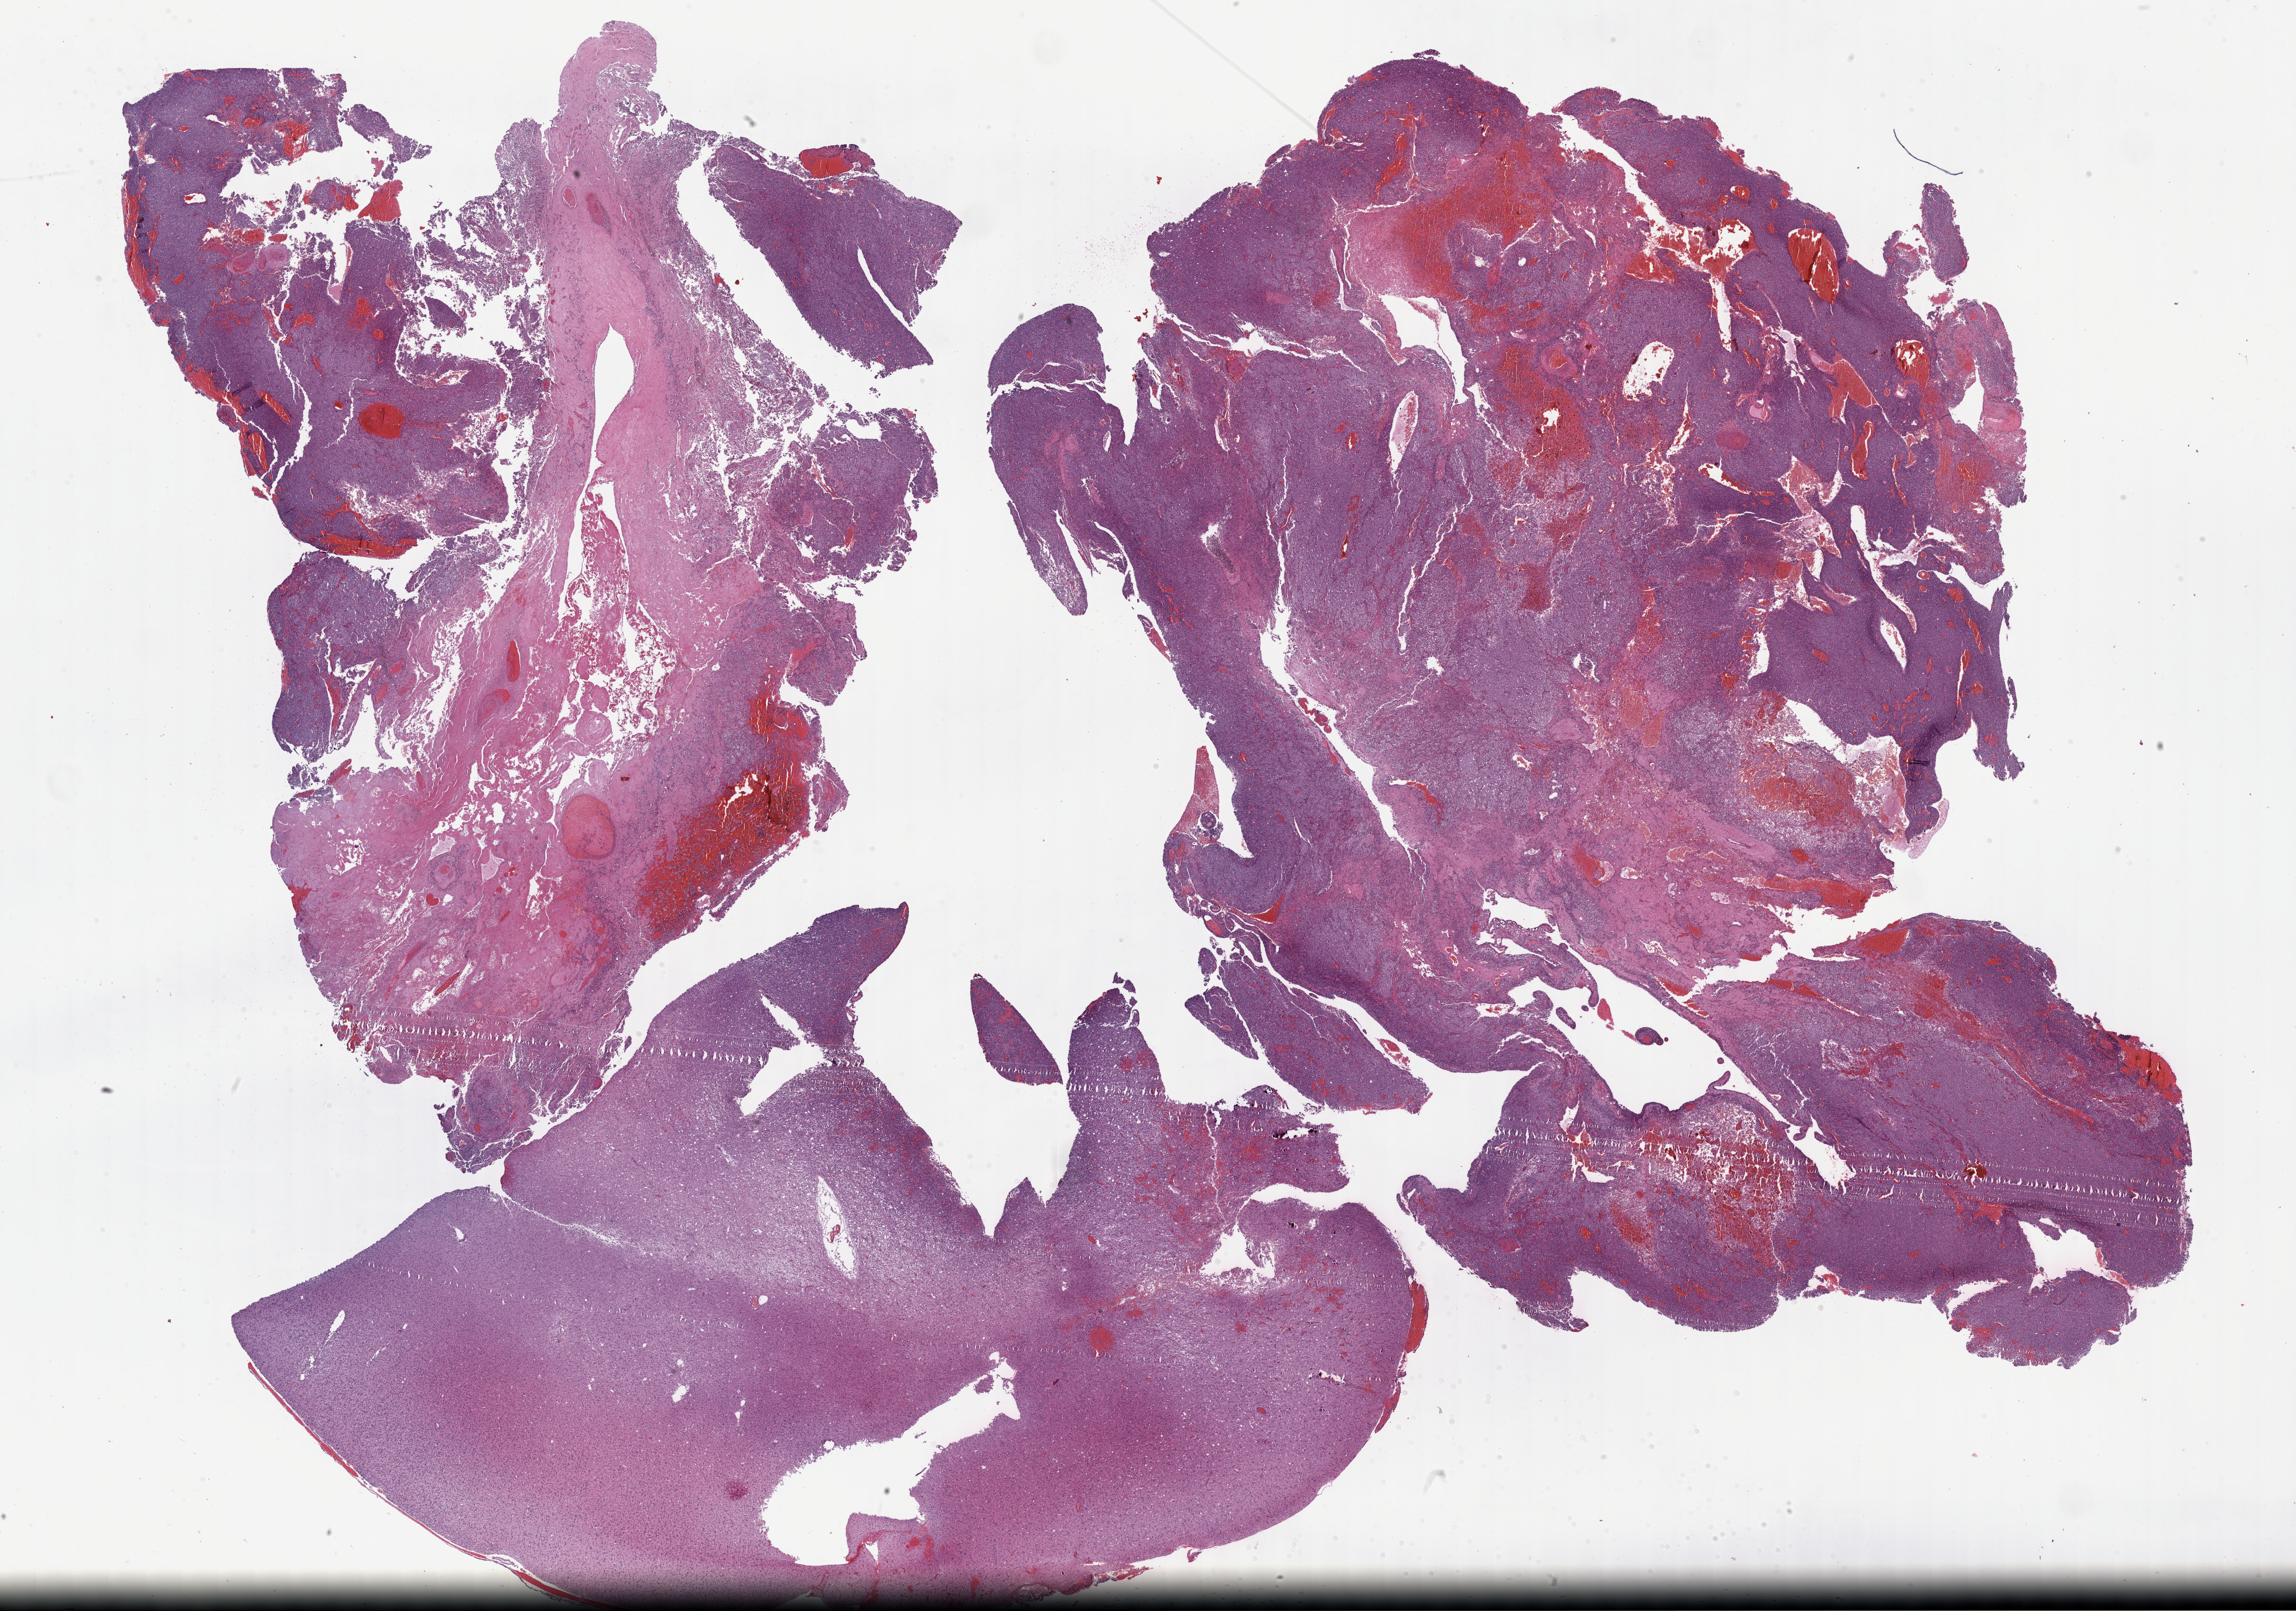
Digitized H&E-stained tissue section (whole slide), whole scanned area (about 31.7 x 22.2 mm) shown as a low-resolution overview; formalin-fixed paraffin-embedded (FFPE) diagnostic section; brain, primary tumour sample. Patient: male, age at initial diagnosis 33 years. Histologic grade: G3 (poorly differentiated).
Histologic diagnosis: Oligodendroglioma, anaplastic. Laterality: left.